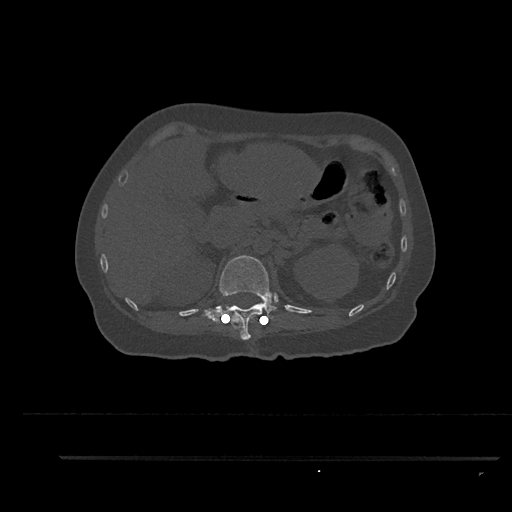
CT including the spine, one axial slice. Slice 253 of 797 in the series (ordered by position). Bone window (W 1800 / L 400 HU). 0.5 mm slice thickness. 512 × 512 image matrix, field of view 408 × 408 mm. Patient: female, 44 years. From the clinical record (not read from this slice): primary cancer: renal; vertebrae with lytic lesions (as recorded): L1.
Structures marked on this image (semi-automatic segmentation, software-assisted and operator-edited):
- T12 vertebra: bounding box <202,255,273,340> (left, top, right, bottom; pixels)